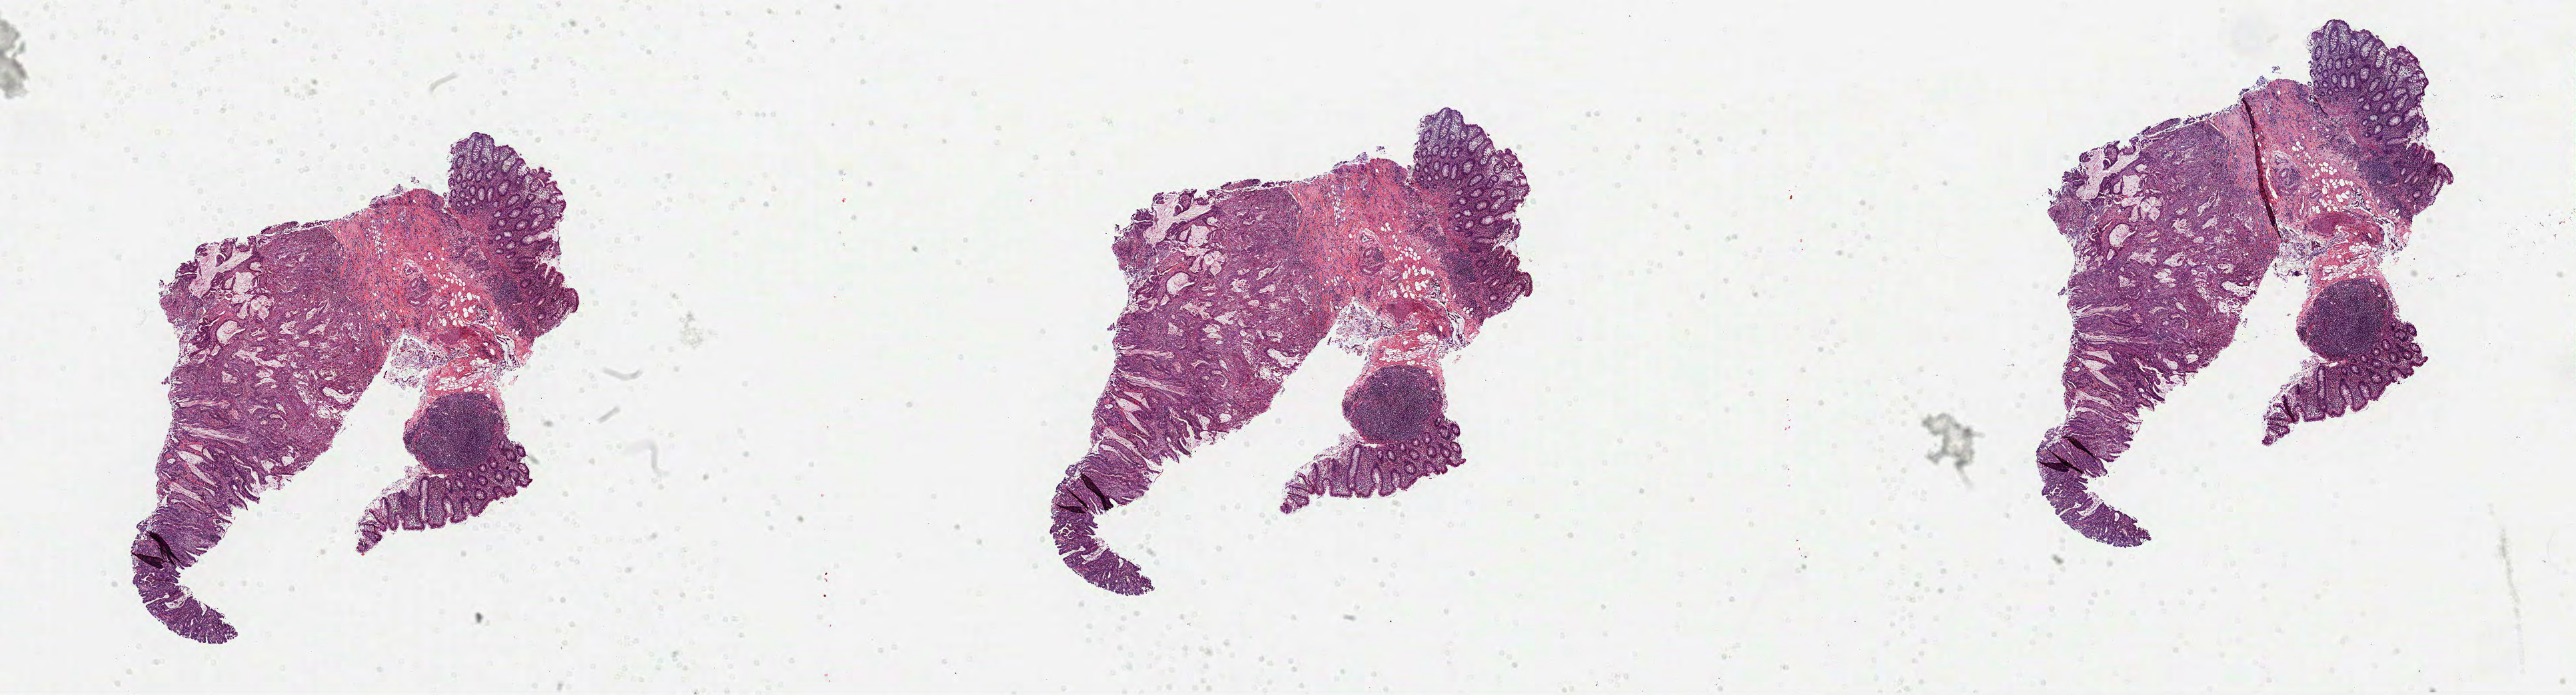
H&E-stained whole-slide image — a low-resolution overview of the entire scanned area, about 31.2 x 8.4 mm (from a 40x scan); formalin-fixed paraffin-embedded (FFPE) diagnostic section; colon, primary tumour sample. Female, age 80 years at initial diagnosis.
AJCC pathologic stage: IIA. TNM: T3 N0 M0. Pathologic diagnosis: Adenocarcinoma, NOS (ascending colon). Lymph nodes positive (case pathology): 0 of 21 examined.